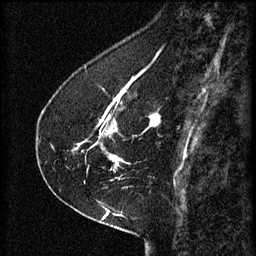
Breast MRI (dynamic contrast-enhanced), one sagittal slice; position 21 of 60 along the scan axis; 3 images stored at this slice position (order not interpretable as contrast timing); 1.5 T; TE 4.2 ms, TR 8.2 ms; 2 mm slice thickness; 256 × 256 image matrix, field of view 180 × 180 mm. Patient: female, 41 years.
Outlined on this slice (semi-automatic segmentation, software-assisted and operator-edited):
- analysis volume of interest (the breast-tissue region the enhancement analysis was run in; not a lesion): bounding box [x1, y1, x2, y2] px = [74, 92, 157, 173]
- tumour enhancement mask (voxels above the 70 % enhancement threshold inside the analysis volume of interest): [74, 98, 157, 167]